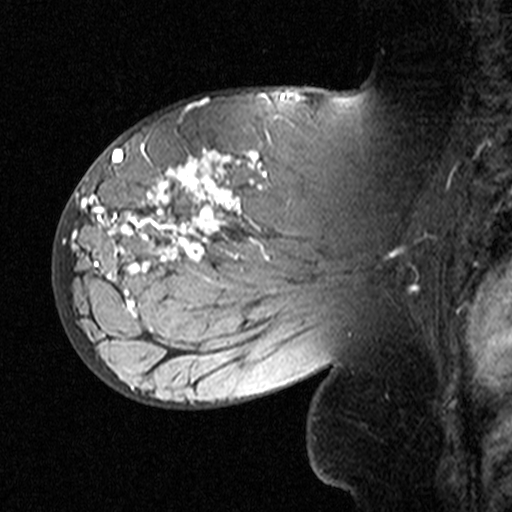
Breast MRI (dynamic contrast-enhanced), one sagittal slice. Slice 25 of 44 in the series (ordered by position). Dynamic contrast-enhanced study with each time point stored as its own series, time point 2 of 3 at this slice position (early post-contrast, ordered by acquisition time). 1.5 T. TE 4.5 ms, TR 11 ms. 512 × 512 image matrix, field of view 200 × 200 mm. Patient: female, 53 years. Case-level facts recorded for this patient, not image findings: setting: breast cancer imaged before/during neoadjuvant chemotherapy; receptor status: HR-positive, HER2-negative.
Structures marked on this image (semi-automatically segmented with operator editing):
- analysis volume of interest (the breast-tissue region the enhancement analysis was run in; not a lesion): bounding box <76,140,311,353> (left, top, right, bottom; pixels)
- tumour enhancement mask (voxels above the 90 % enhancement threshold inside the analysis volume of interest): <95,149,266,316>